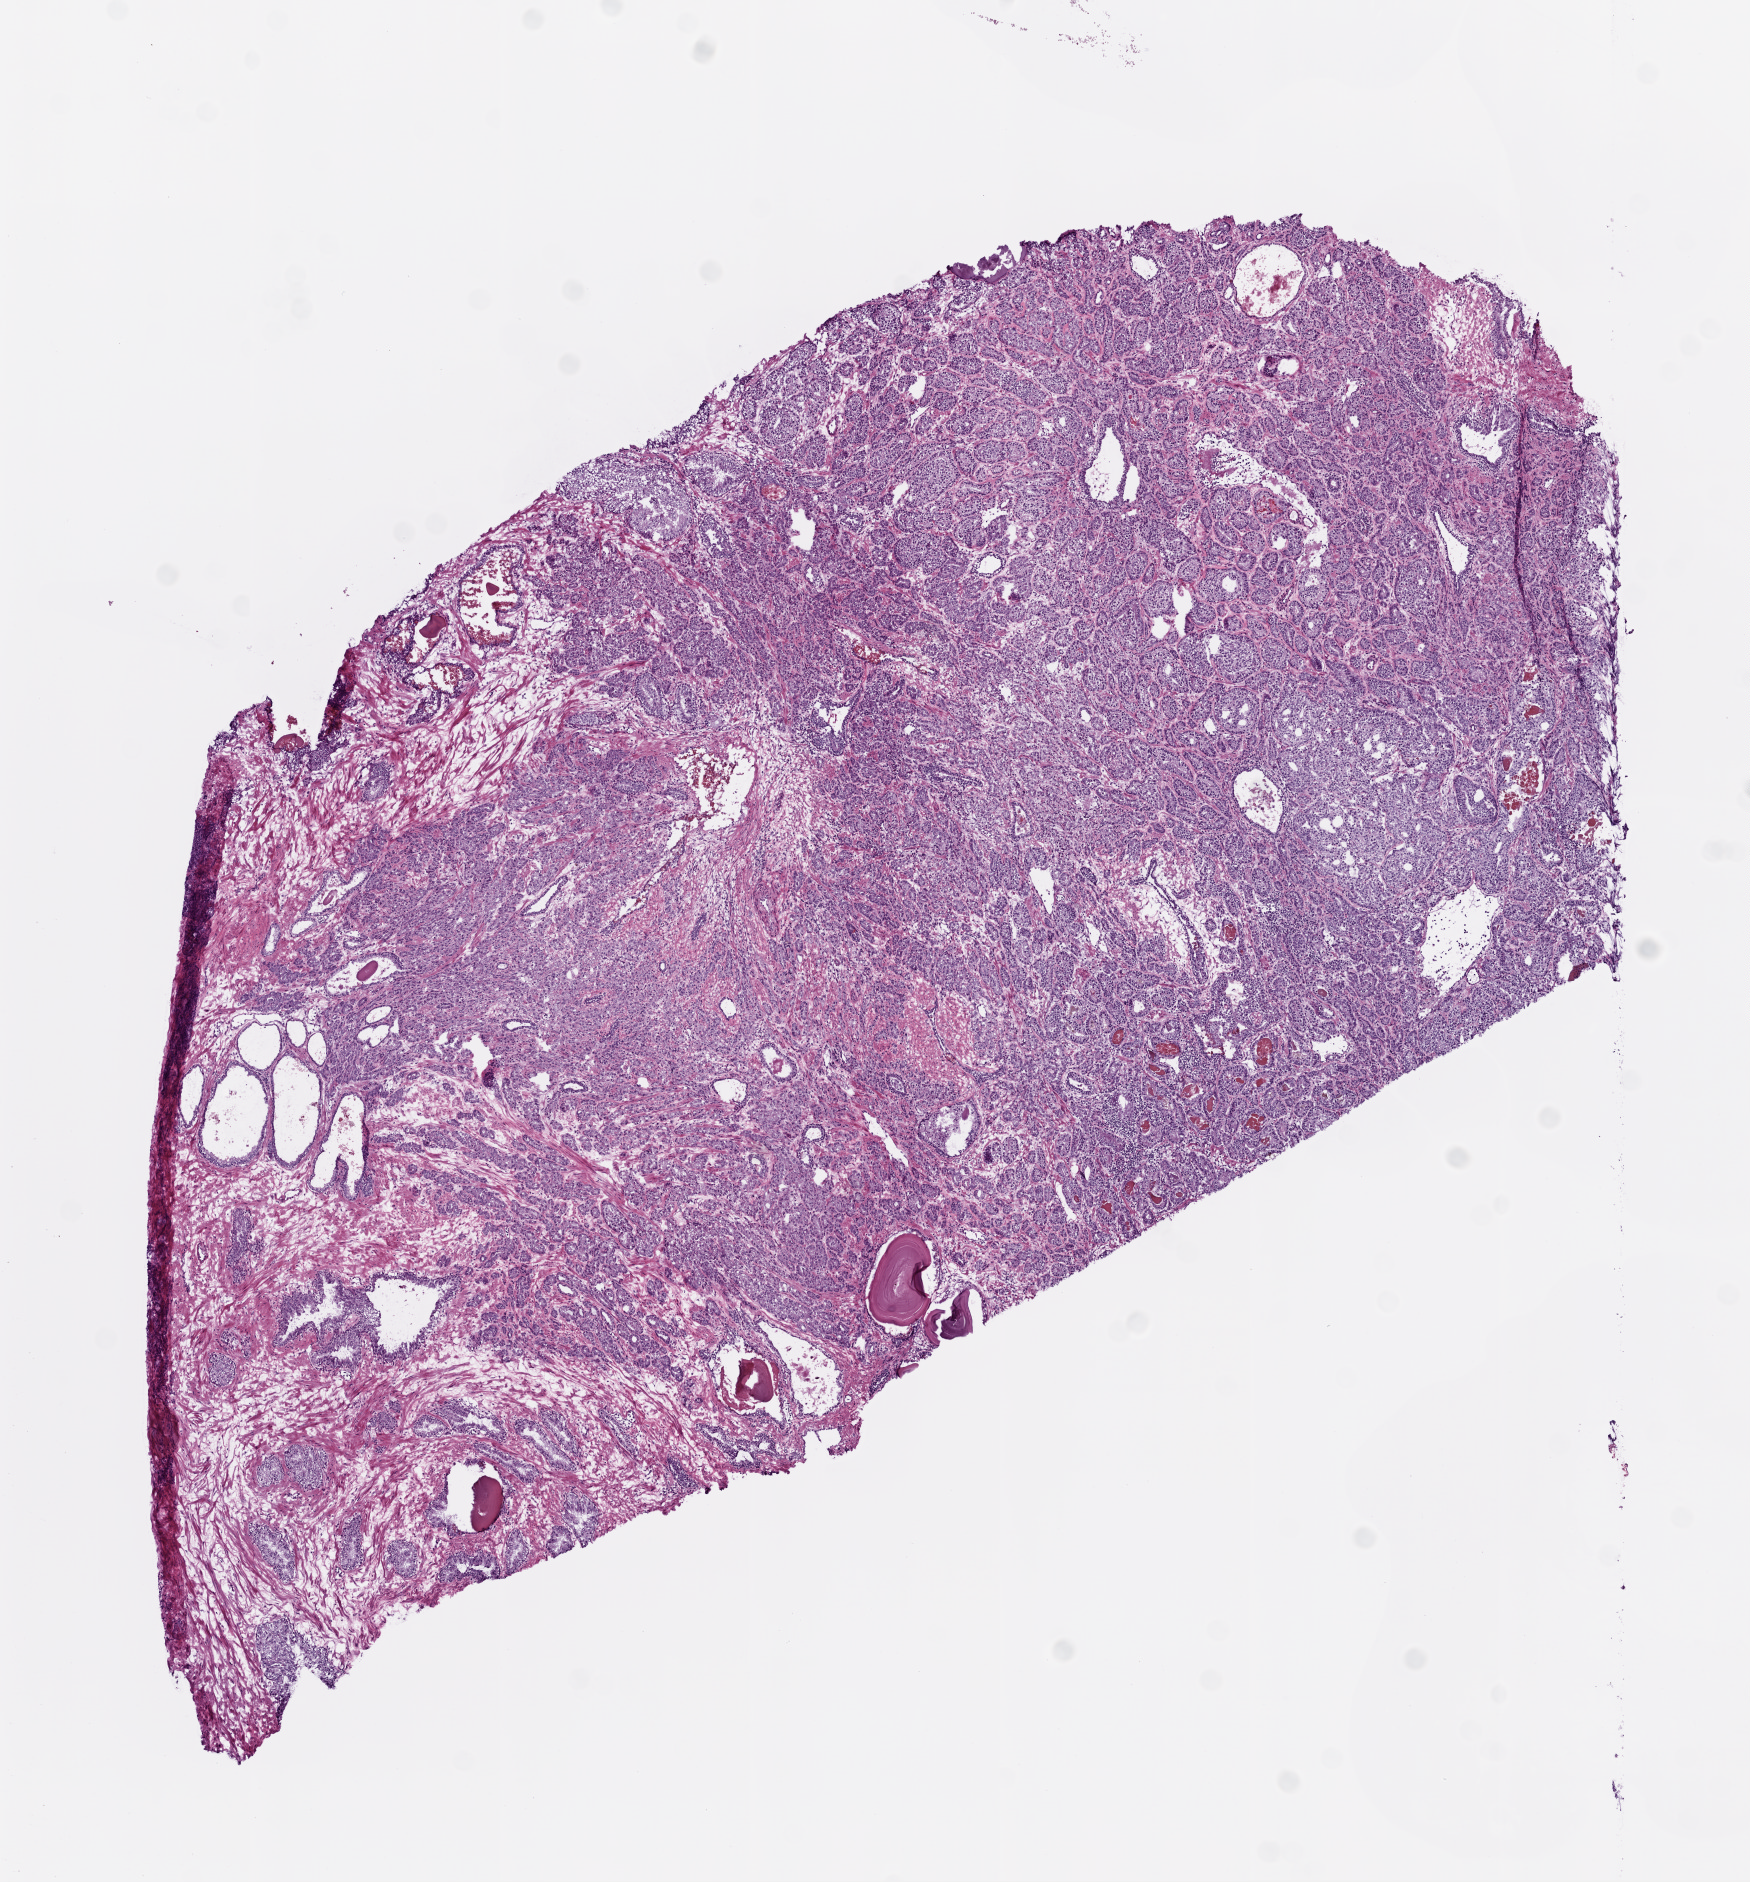
Hematoxylin and eosin (H&E) stained whole-slide image, low-resolution overview of the scanned area, about 7.0 x 7.6 mm. Frozen section from the top of the tissue portion. Sample: primary tumour, prostate. Patient: male, age at initial diagnosis 70 years. Gleason score: 9 (4+5). Pathologist review of this section (percent, as recorded): tumour cells 70%, tumour nuclei 80%, normal cells 15%, stromal cells 15%, necrosis 0%. Inflammatory infiltration, as recorded: lymphocyte infiltration 0%, monocyte infiltration 0%, neutrophil infiltration 0%.
• laterality: bilateral
• lymph nodes positive (case pathology): 3 of 10 examined
• pathologic diagnosis: Acinar cell carcinoma (prostate gland)